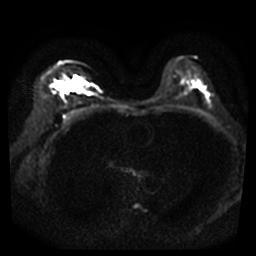
Breast MRI, one axial slice; diffusion-weighted series; image 2 of 4 stored at this slice position (different b-values; order by instance number); 3 T; 5 mm slice thickness; 256 × 256 image matrix. Female patient.
Annotated regions visible in this slice (outlined manually by an expert reader):
- tumour on diffusion-weighted imaging: bounding box (x1, y1, x2, y2) in pixels: (63, 81, 77, 92)